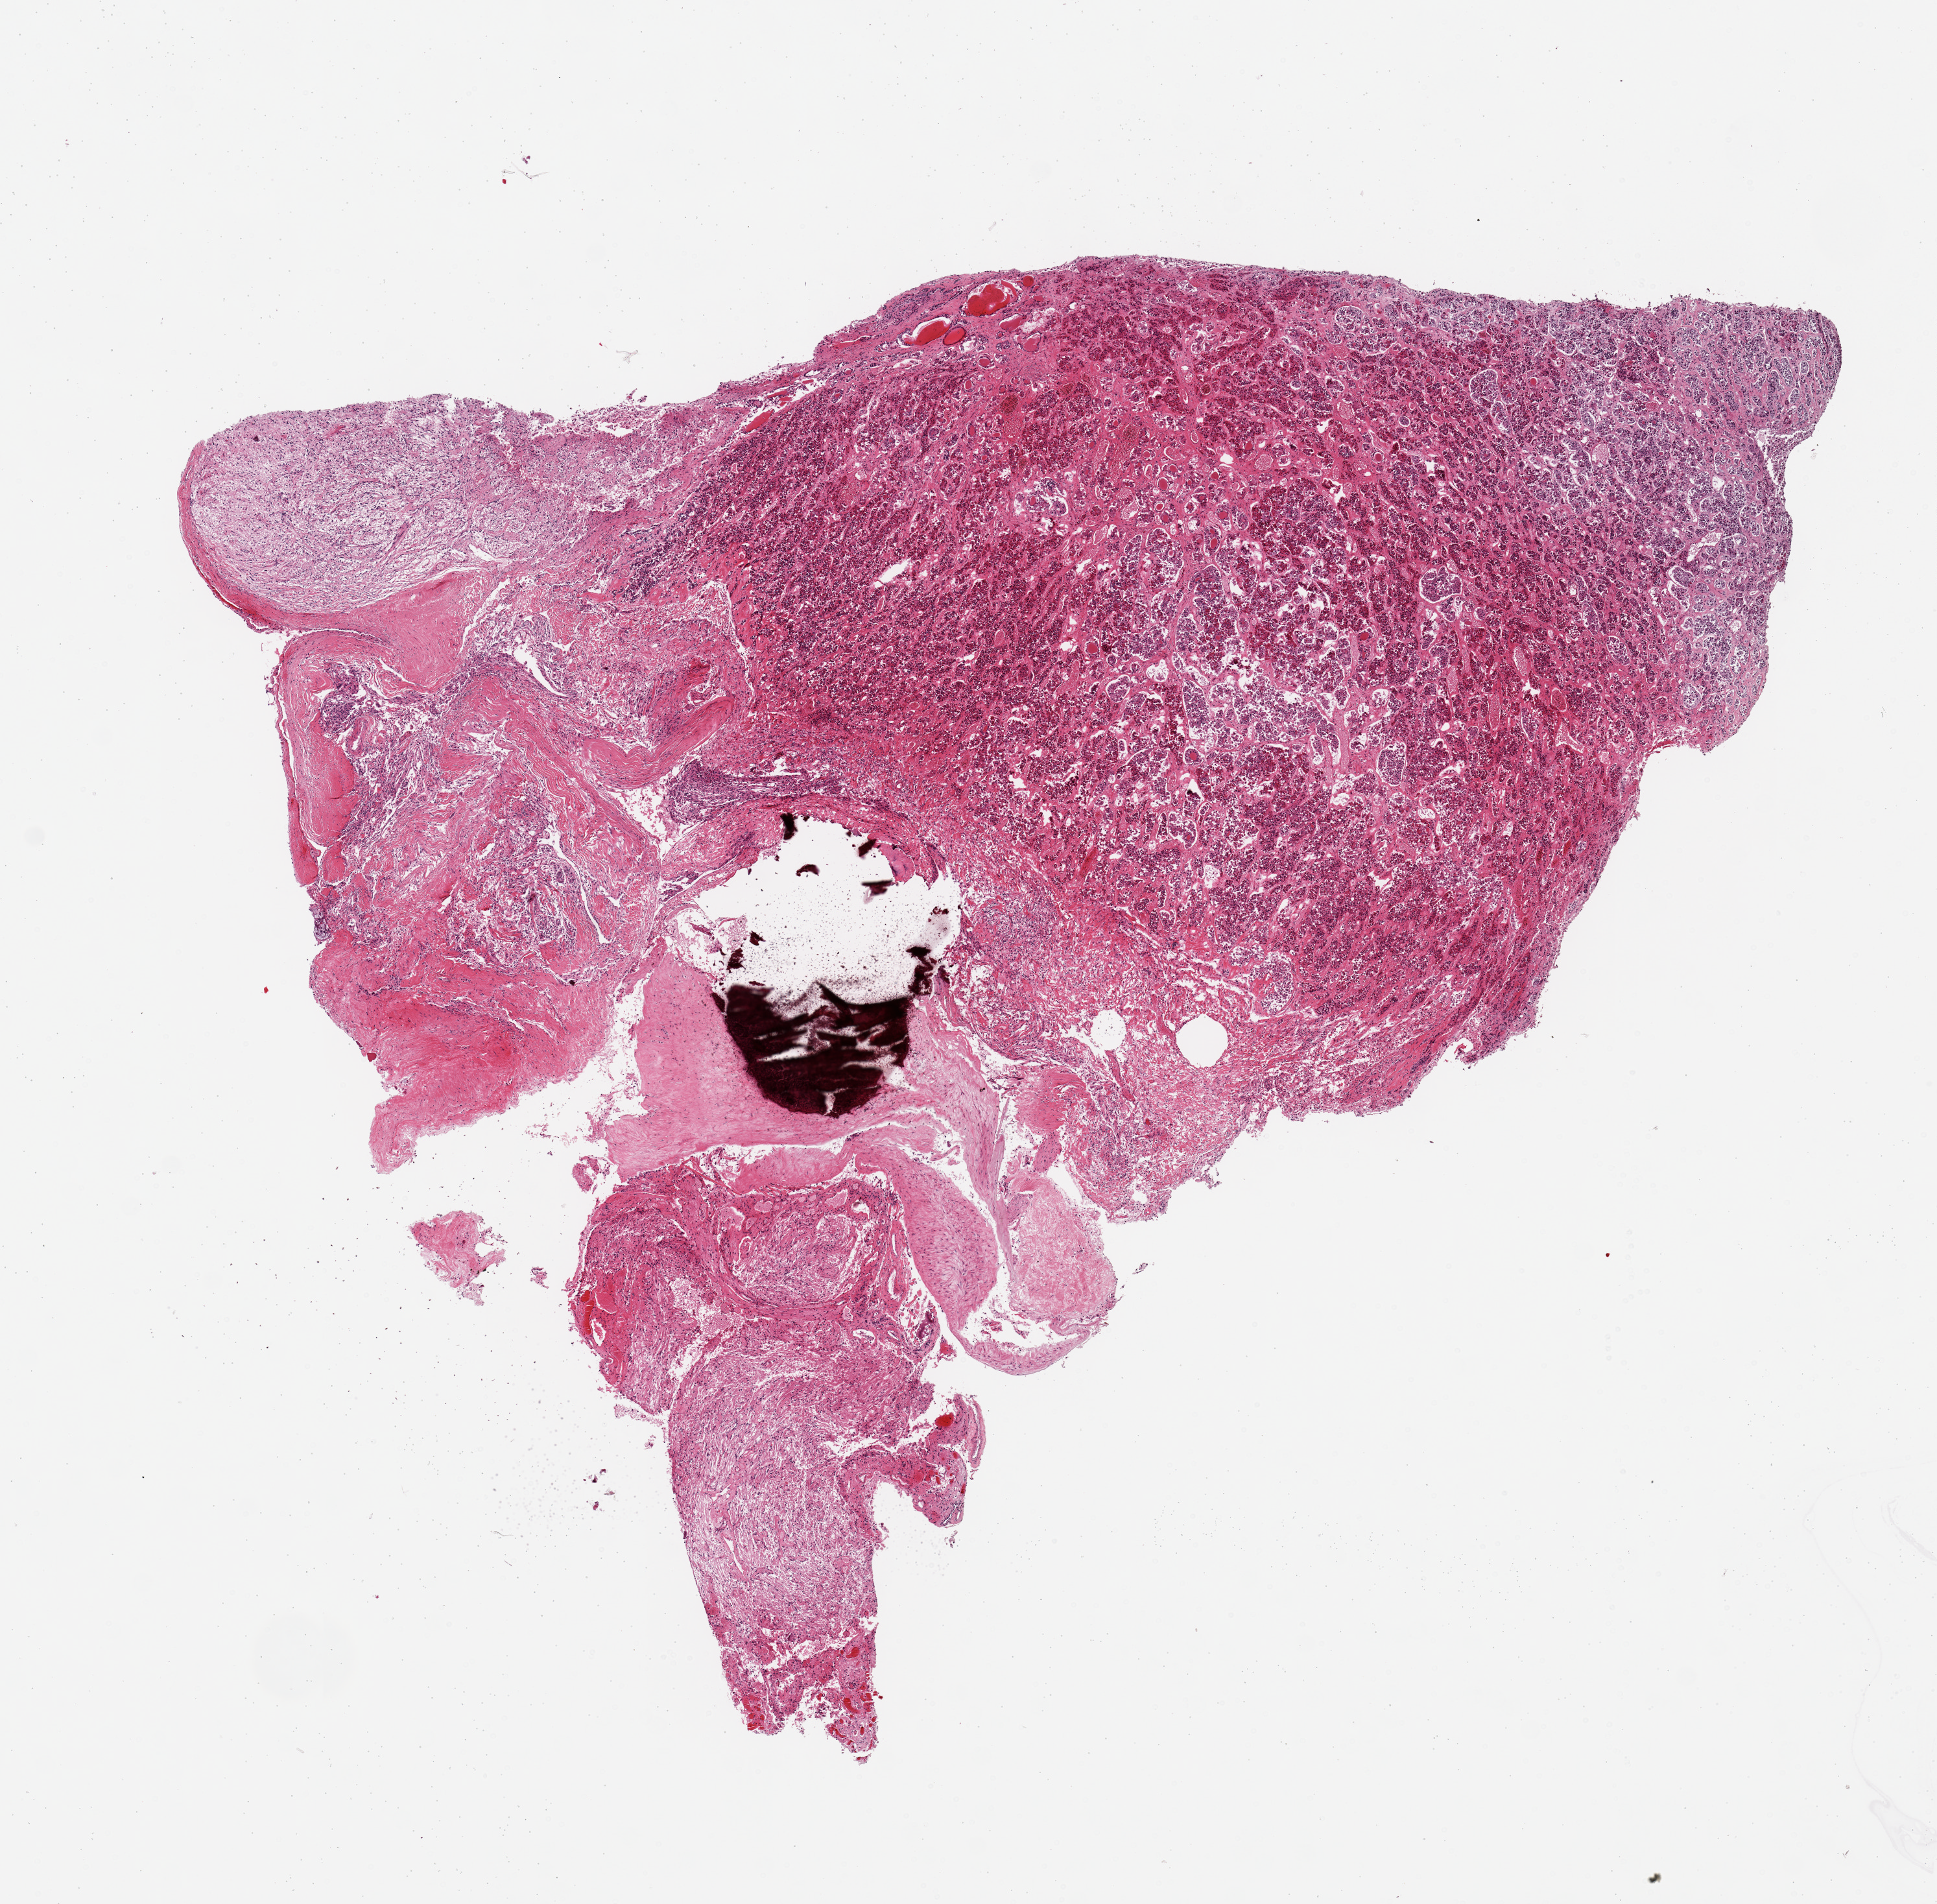
H&E whole-slide image — whole scanned area (about 11.8 x 11.6 mm) shown as a low-resolution overview; PAXgene-fixed paraffin-embedded (PFPE) section; section of pituitary (target tissue); tissue donor sample. Donor sex: female.
Review note (as recorded): 1 piece, ~50% neurohypophysis/50% adenohypophysis; ~1.5mm focus of prominent dystrophic calcification at junction of neuro/adenophysis, unknown etiology.